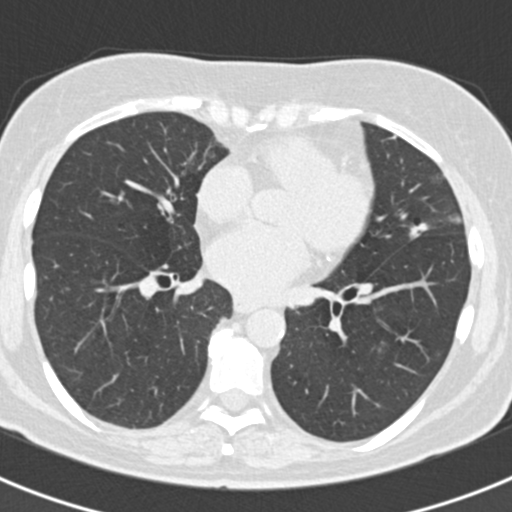
Axial slice from a low-dose chest CT screening exam. Baseline annual screen. Lung window (W 1500 / L -600 HU). Standard (soft-tissue) reconstruction kernel (B30f). 120 kVp. Slice 112 of 184 in the series. Female participant, aged 60 years at enrolment. Current smoker at enrolment.
Lesion marked by an expert reader, box from (x=398, y=215) to (x=436, y=248) px. The screening reader recorded 3 non-calcified nodules or masses ≥4 mm on this exam (lingula, left lower lobe, lingula); which of them this box marks is not recorded. Official screen result: positive, change unspecified: nodule(s) >= 4 mm or enlarging nodule(s), mass(es), or other non-specific abnormalities suspicious for lung cancer. Later outcome: lung cancer diagnosed 886 days after this screen — non-small cell carcinoma, left upper lobe, poorly differentiated (G3), stage IB (AJCC 6th edition), 7 mm at pathology.